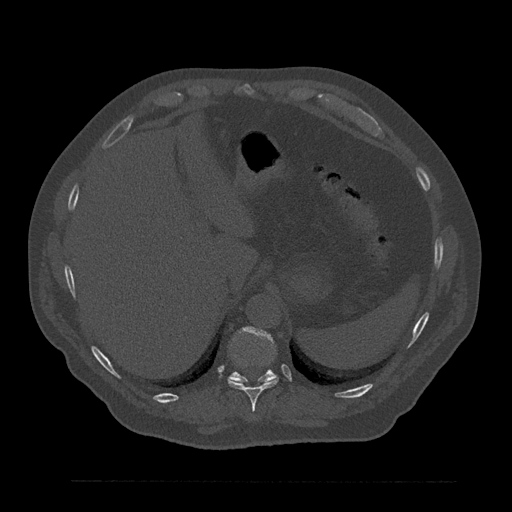
CT including the spine, one axial slice; slice 328 of 797 in the series (ordered by position); reconstruction kernel Br40s/3; 120 kVp; bone window (W 1800 / L 400 HU); 0.5 mm slice thickness; 512 × 512 image matrix, field of view 430 × 430 mm. Male patient, age 61 years. From the clinical record (not read from this slice): primary cancer: prostate.
Outlined on this slice (semi-automatically segmented with operator editing):
- T10 vertebra: box from (x=228, y=377) to (x=278, y=411) px
- T11 vertebra: (x=229, y=327)–(x=276, y=382)